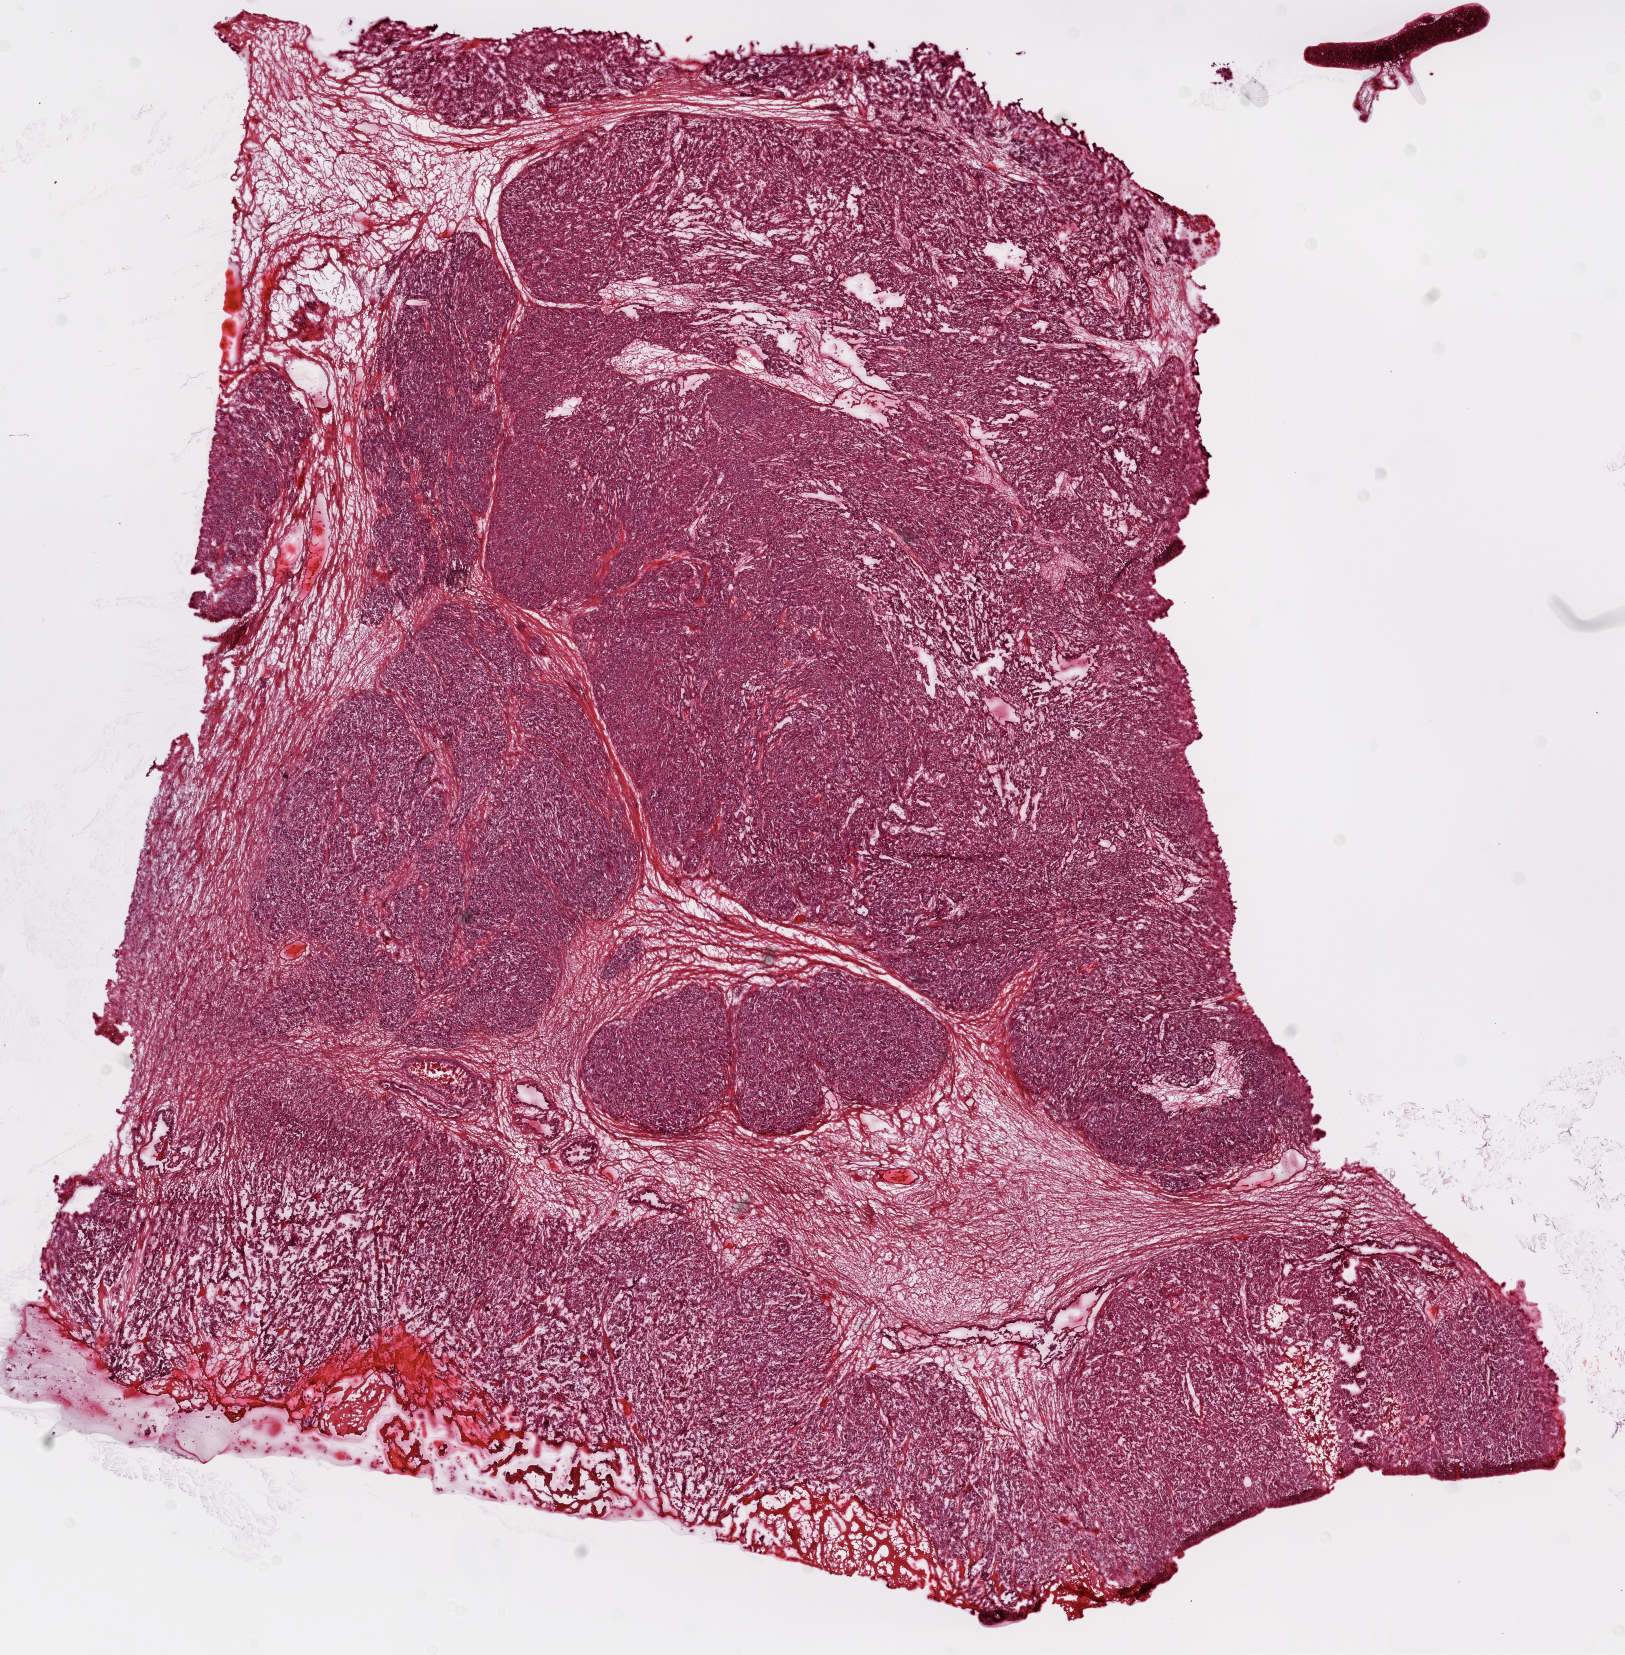
Digitized Hematoxylin and eosin (H&E) stained tissue section (whole slide) — low-resolution overview of the scanned area, about 13.0 x 13.3 mm, frozen section from the top of the tissue portion, ovary, primary tumour sample. Patient: female, age at initial diagnosis 66 years. Histologic grade: G3 (poorly differentiated). Composition of this section per pathologist review: tumour cells 50%, tumour nuclei 90%, normal cells 45%, stromal cells 0%, necrosis 5%.
Histologic diagnosis: Serous cystadenocarcinoma, NOS. FIGO stage: IIIC.